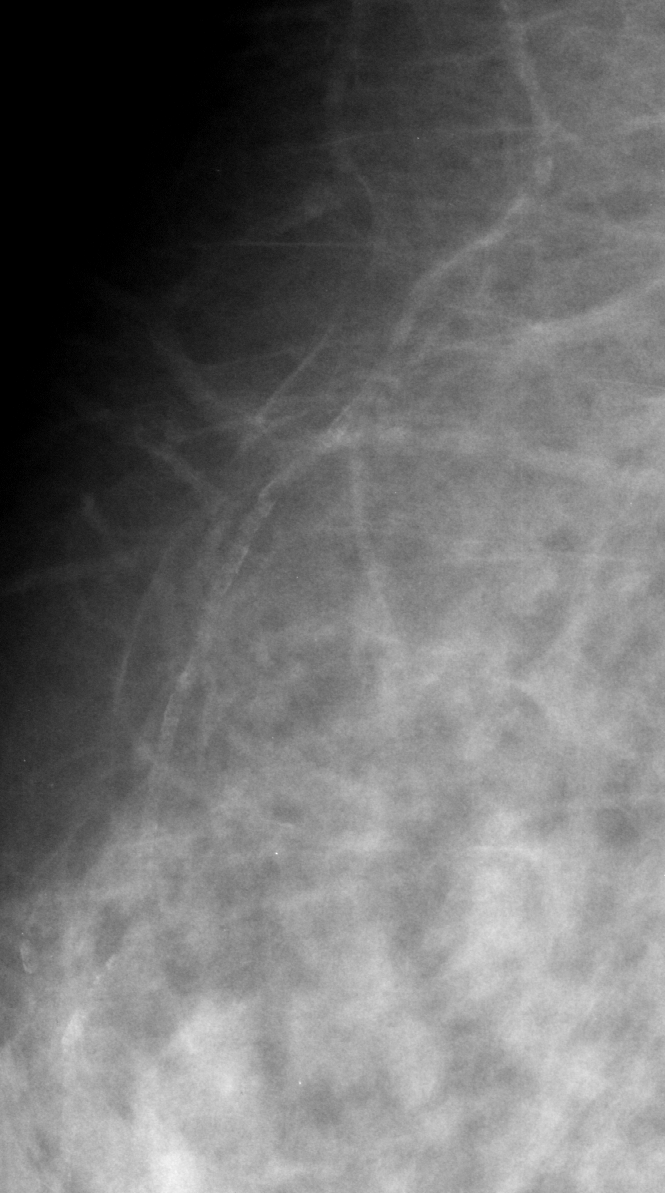
Crop from a digitized film mammogram around one marked abnormality; right breast; MLO view; BI-RADS breast density category 3 (scale 1–4).
- Calcifications, morphology vascular; BI-RADS assessment category 2; subtlety rating 3 on a 1 (subtle) to 5 (obvious) scale; benign without callback (not worked up further).